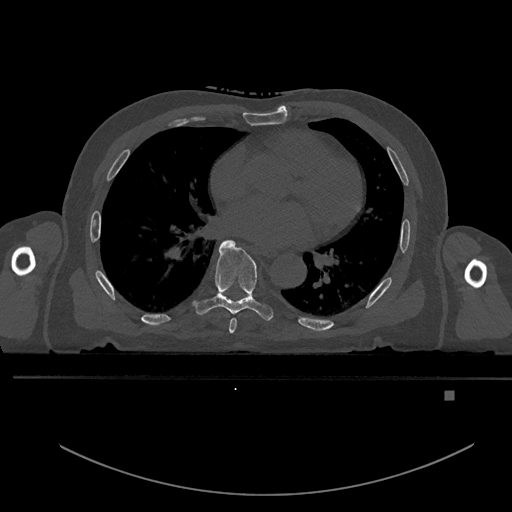
CT including the spine, one axial slice. Position 257 of 969 along the scan axis. Bone window (W 1800 / L 400 HU). 0.5 mm slice thickness. 512 × 512 image matrix. Patient: male, 82 years. From the clinical record (not read from this slice): primary cancer: prostate.
Annotated regions visible in this slice (semi-automatically segmented with operator editing):
- T6 vertebra: bounding box [x1, y1, x2, y2] px = [229, 318, 237, 334]
- T7 vertebra: [193, 240, 273, 321]
- T8 vertebra: [226, 295, 254, 299]